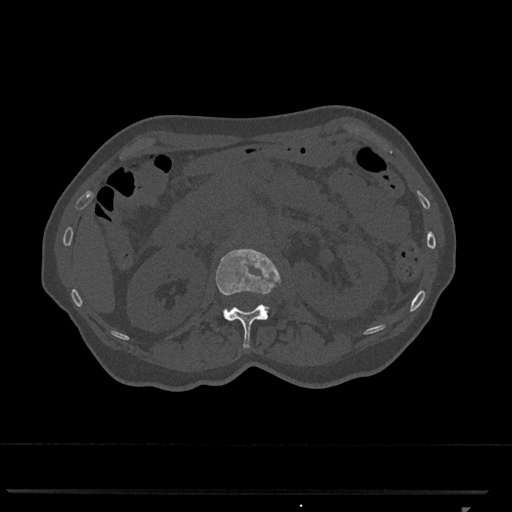
CT including the spine, one axial slice; slice 393 of 793 in the series (ordered by position); reconstruction kernel Br40s/3; bone window (W 1800 / L 400 HU); 0.5 mm slice thickness; 512 × 512 image matrix, field of view 380 × 380 mm. Patient: female, 62 years. From the clinical record (not read from this slice): primary cancer: renal.
Annotated regions visible in this slice (semi-automatically segmented with operator editing):
- L1 vertebra: bounding box [x1, y1, x2, y2] px = [215, 248, 281, 349]